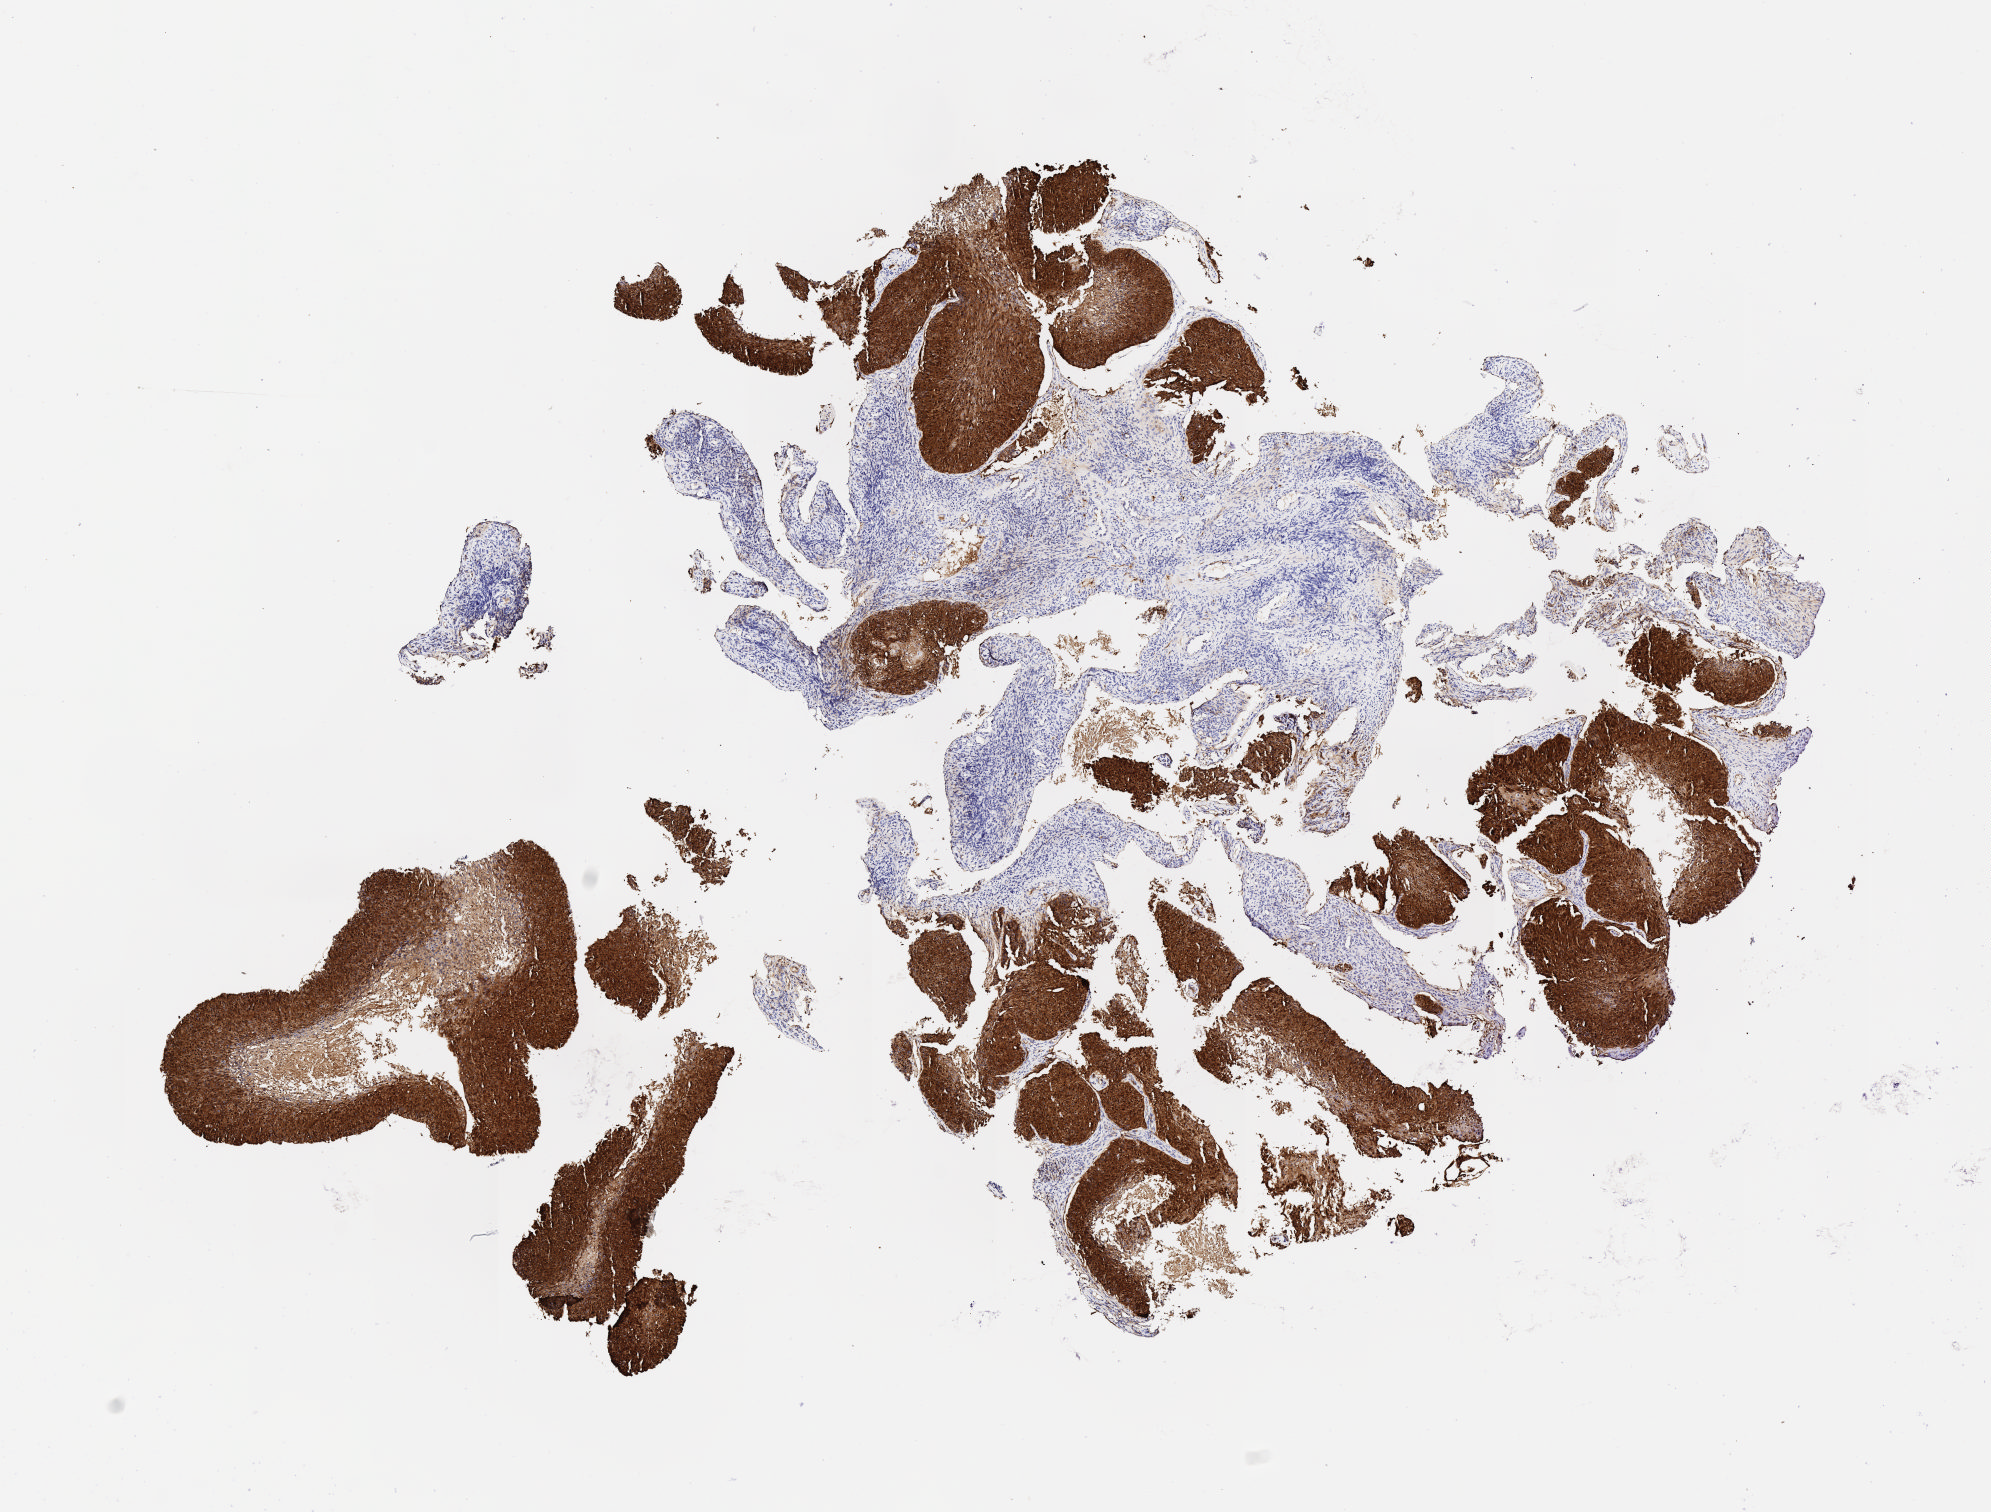
Whole-slide image, immunohistochemical stain for p16 (p16INK4a) — low-resolution overview of the scanned area, about 8.1 x 6.1 mm; tumor tissue; anatomic site: cervix. Patient: female, 48 years old.
• histologic diagnosis: Squamous cell carcinoma, keratinizing, NOS